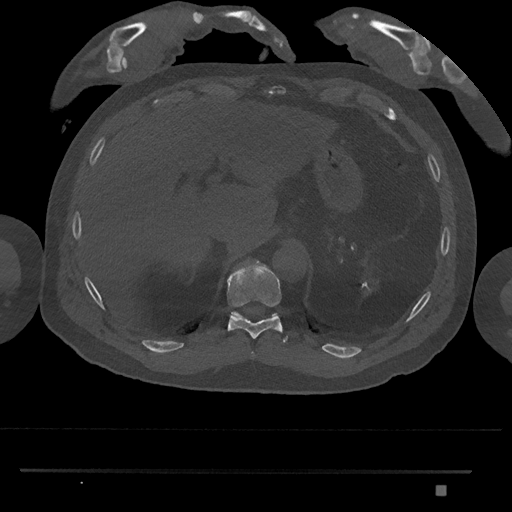
CT including the spine, one axial slice; slice 993 of 1134 in the series (ordered by position); reconstruction kernel Br40s/3; 120 kVp; bone window (W 1800 / L 400 HU); 0.5 mm slice thickness; 512 × 512 image matrix. Patient: male, 65 years. Case-level facts recorded for this patient, not image findings: primary cancer: prostate.
Outlined on this slice (semi-automatic segmentation, software-assisted and operator-edited):
- T10 vertebra: bounding box (x1, y1, x2, y2) in pixels: (227, 261, 287, 342)
- T11 vertebra: (231, 311, 278, 318)
- T9 vertebra: (251, 352, 255, 357)